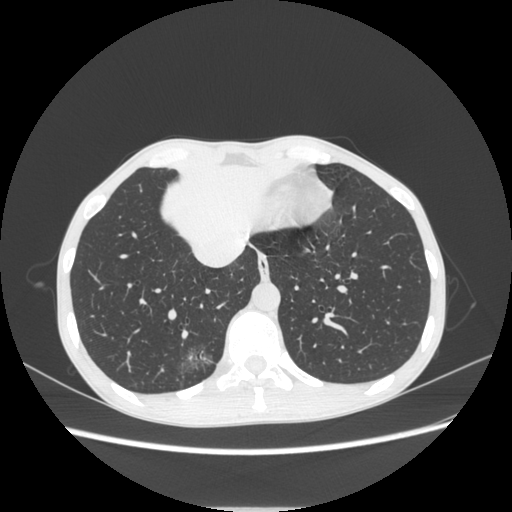
Chest CT, one axial slice; position 78 of 272 along the scan axis; reconstruction kernel STANDARD; lung window (W 1500 / L -600 HU); 512 × 512 image matrix, field of view 350 × 350 mm. Female patient, age 51 years. From the clinical record (not read from this slice): clinical TNM (as recorded): T1c N0 M0.
Structures marked on this image (rectangle marked by the reading radiologist):
- lung tumour (recorded histology: adenocarcinoma): box from (x=174, y=339) to (x=213, y=387) px